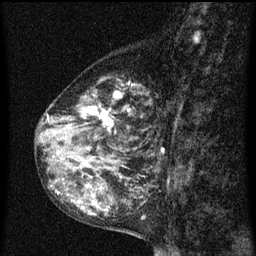
Breast MRI (dynamic contrast-enhanced), one sagittal slice. Position 28 of 60 along the scan axis. Dynamic contrast-enhanced series, image 2 of 3 at this slice position (ordered by acquisition). 1.5 T. TE 4.2 ms, TR 8 ms. 2 mm slice thickness. 256 × 256 image matrix. Patient: female, 55 years.
Annotated regions visible in this slice (semi-automatic segmentation, software-assisted and operator-edited):
- analysis volume of interest (the breast-tissue region the enhancement analysis was run in; not a lesion): box from (x=36, y=78) to (x=157, y=151) px
- tumour enhancement mask (voxels above the 70 % enhancement threshold inside the analysis volume of interest): (x=48, y=84)–(x=131, y=139)